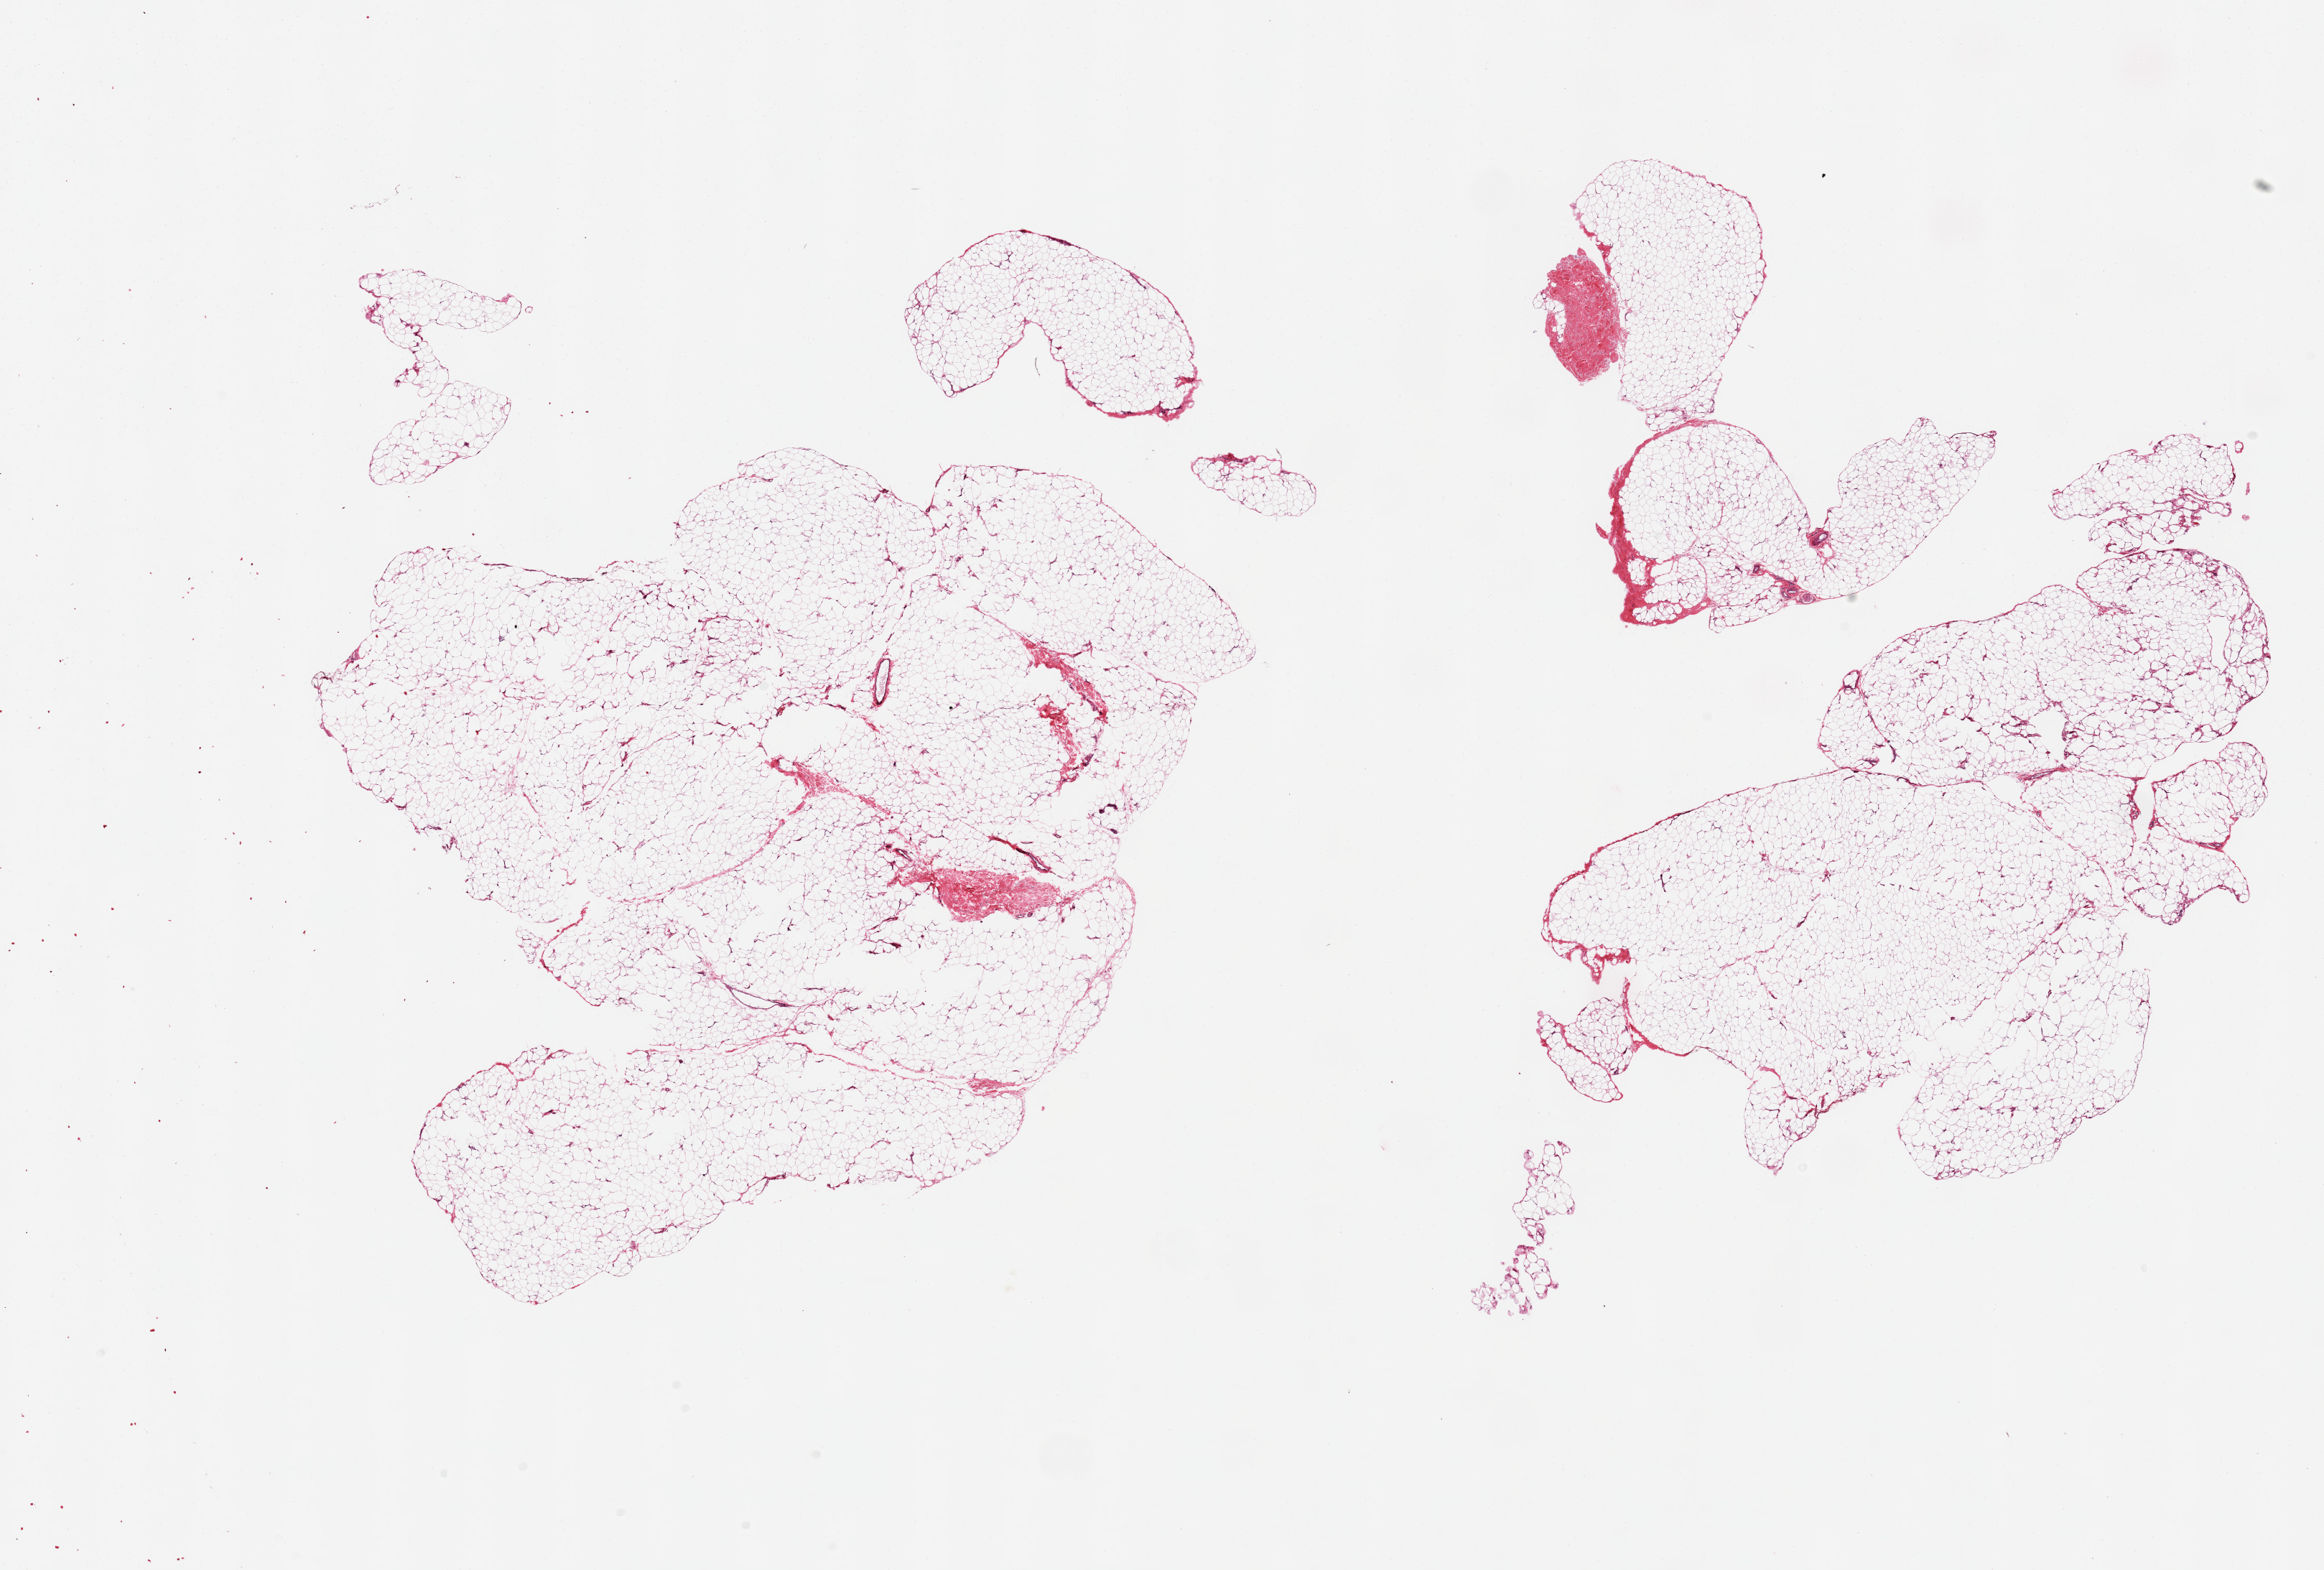
Whole-slide image, hematoxylin and eosin (H&E) stain — a low-resolution overview of the entire scanned area, about 25.6 x 17.3 mm (slide scanned at 20x), PAXgene-fixed, paraffin-embedded tissue, sampled site (target tissue): adipose tissue, donor tissue sample. Donor: male.
Review note (as recorded): 2 fragmented pieces; mature adipose tissue.